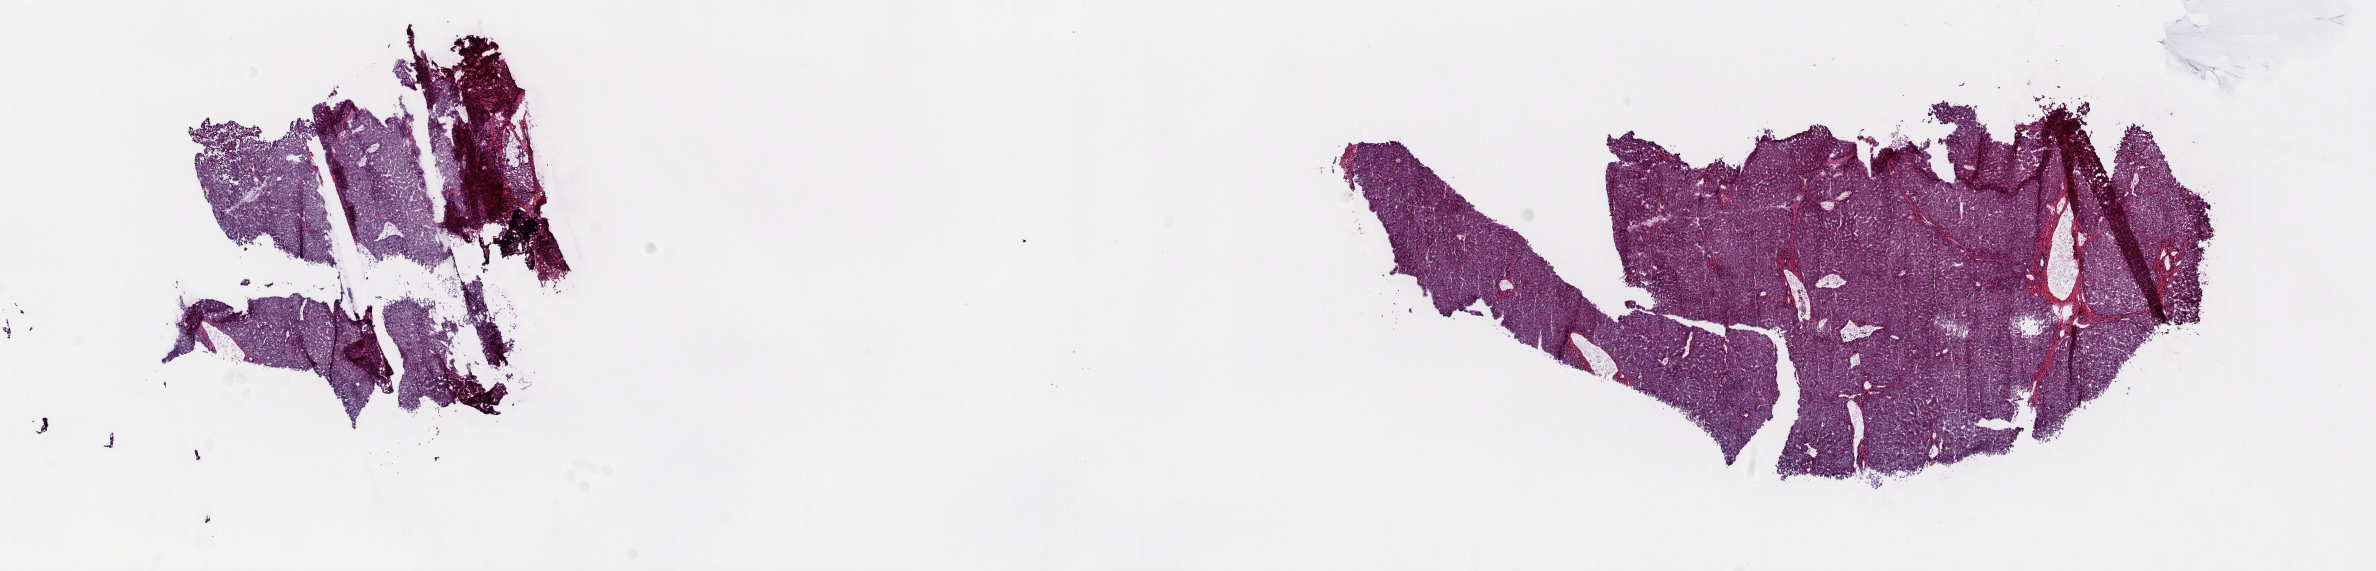
Whole-slide histology image, H&E-stained — shown as a low-resolution overview of the whole scanned area (about 18.8 x 4.5 mm); frozen section from the top of the tissue portion; solid tissue normal (non-tumour tissue) sample from the liver. Male patient; age at initial diagnosis 23 years. Pathologist review of this section (percent, as recorded): tumour cells 0%, tumour nuclei 0%, normal cells 75%, stromal cells 25%, necrosis 0%. Infiltration values recorded for this section: lymphocyte infiltration 8%, monocyte infiltration 0%, neutrophil infiltration 0%.
This section: solid tissue normal sample (biorepository sample class). Patient diagnosis: Hepatocellular carcinoma, NOS.